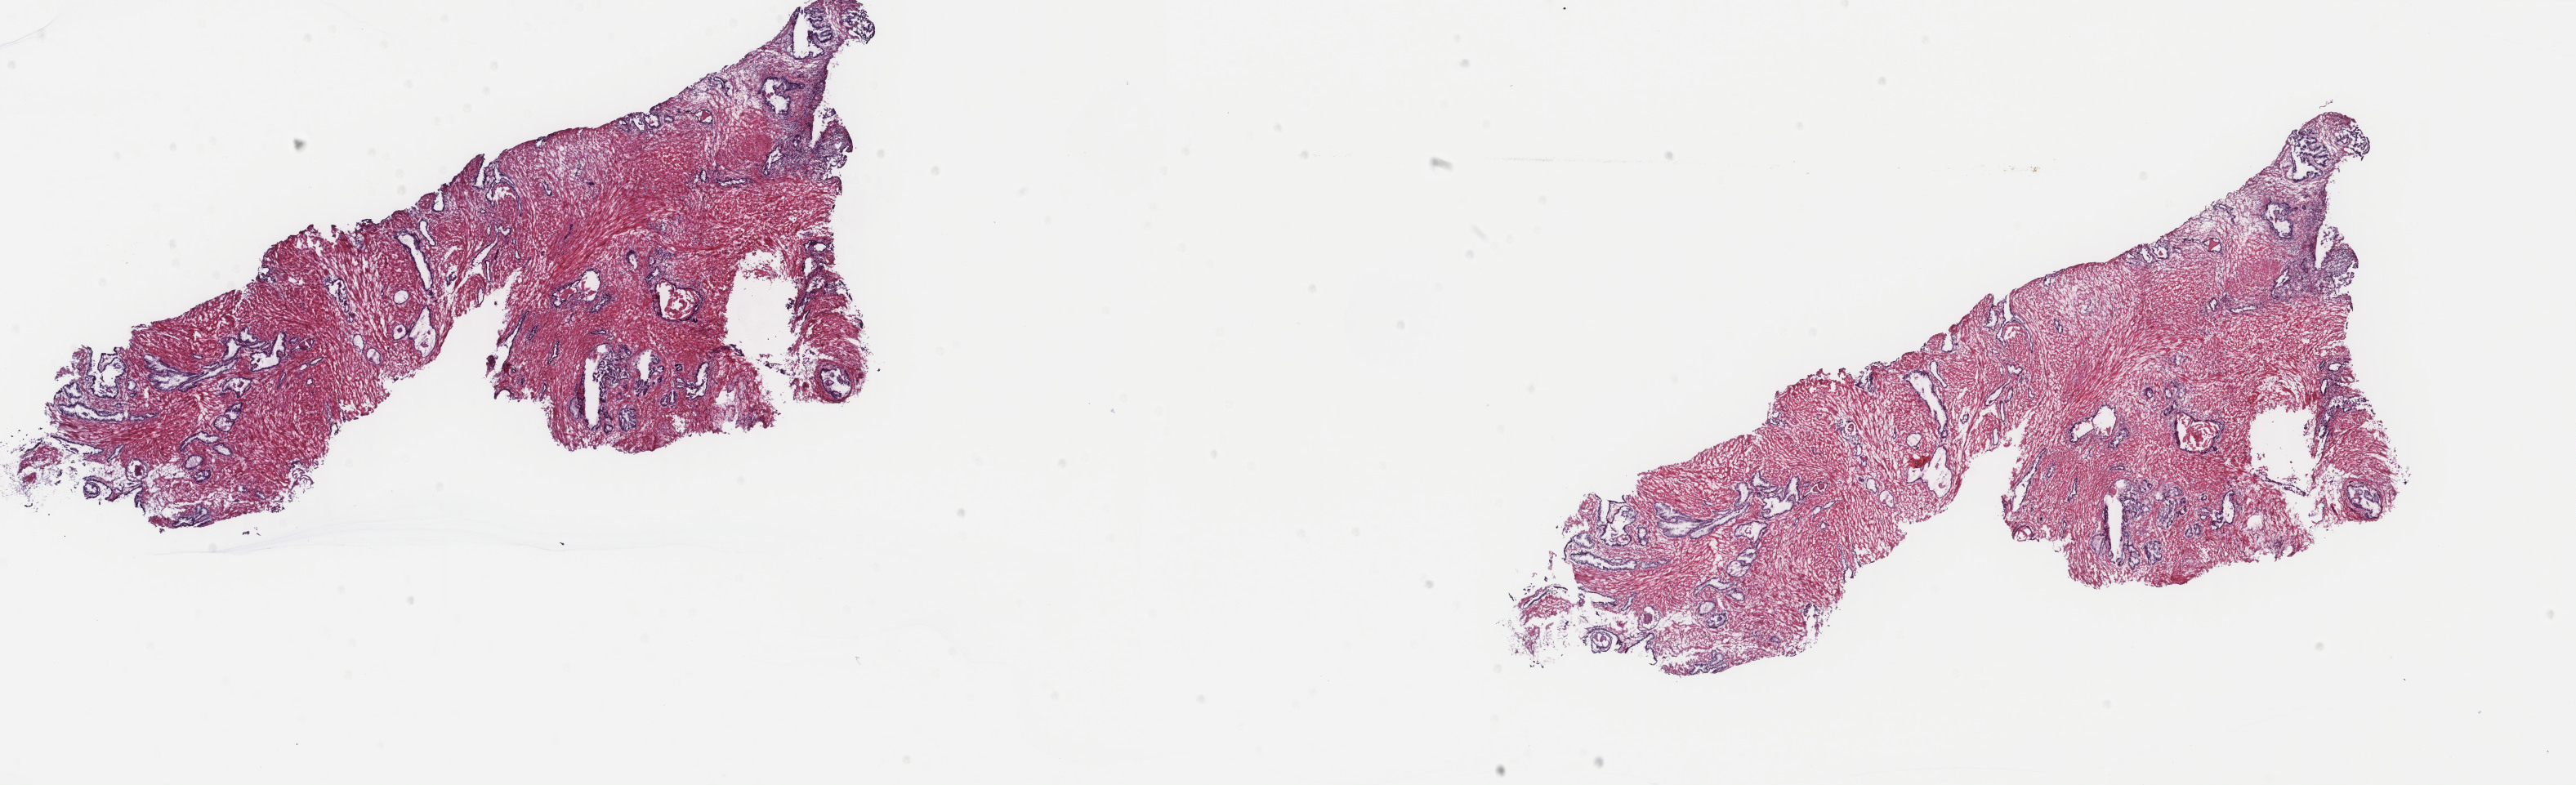
Digitized Hematoxylin and eosin (H&E) stained tissue section (whole slide), whole scanned area (about 25.0 x 7.6 mm, slide scanned at 40x) shown as a low-resolution overview. Frozen section from the top of the tissue portion. Sample: primary tumour, prostate. Patient: male, age at initial diagnosis 60 years. Composition of this section per pathologist review: tumour cells 20%, tumour nuclei 60%.
Histologic diagnosis: Adenocarcinoma, NOS (prostate gland).